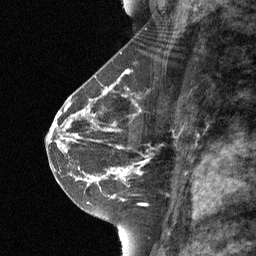
Breast MRI (dynamic contrast-enhanced), one sagittal slice; slice 35 of 64 in the series (ordered by position); dynamic contrast-enhanced study with each time point stored as its own series, time point 2 of 3 at this slice position (early post-contrast, ordered by acquisition time); 1.5 T; TE 4.8 ms, TR 27 ms; 2 mm slice thickness; 256 × 256 image matrix, field of view 180 × 180 mm. Patient: female, 42 years. From the clinical record (not read from this slice): setting: breast cancer imaged before/during neoadjuvant chemotherapy; receptor status: triple-negative.
Structures marked on this image (semi-automatic segmentation, software-assisted and operator-edited):
- analysis volume of interest (the breast-tissue region the enhancement analysis was run in; not a lesion): bounding box (x1, y1, x2, y2) in pixels: (111, 109, 142, 178)
- tumour enhancement mask (voxels above the 90 % enhancement threshold inside the analysis volume of interest): (116, 169, 129, 173)